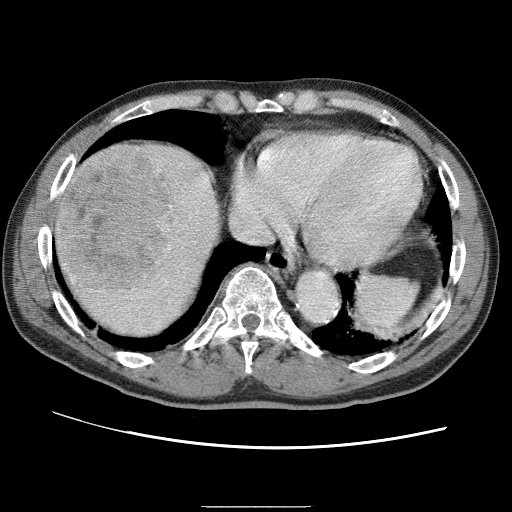
Contrast-enhanced abdominal CT (liver protocol), one axial slice; reconstruction kernel STANDARD; one of 2 acquisitions stored at this slice position; soft-tissue window (W 400 / L 40 HU); 2.5 mm slice thickness; 512 × 512 image matrix, field of view 360 × 360 mm. Case-level facts recorded for this patient, not image findings: diagnosis: hepatocellular carcinoma (patient treated with transarterial chemoembolisation; whether this scan precedes or follows treatment is not stated here); TNM stage (as recorded): Stage-II; Child-Pugh class: A; tumour nodularity: multinodular.
Annotated regions visible in this slice (semi-automatic segmentation, software-assisted and operator-edited):
- liver parenchyma outside the tumour (the mass and vessels are separate outlines, so this box may not span the whole liver): bounding box [x1, y1, x2, y2] px = [52, 142, 224, 338]
- mass: [57, 145, 180, 299]
- liver vessels: [61, 146, 176, 205]